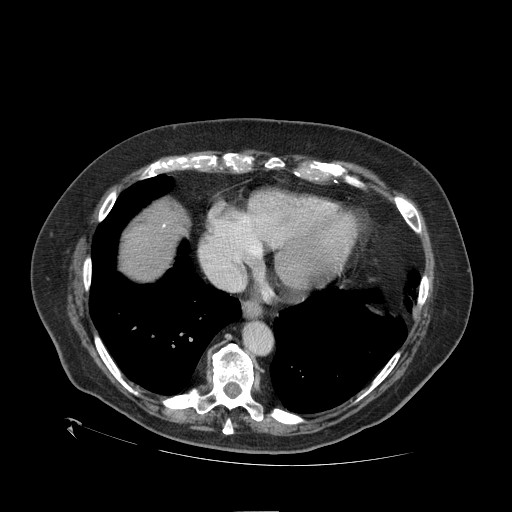
Contrast-enhanced abdominal CT (liver protocol), one axial slice. Slice 98 of 109 in the series (ordered by position). Reconstruction kernel STANDARD. 120 kVp. One of 2 acquisitions stored at this slice position. Soft-tissue window (W 400 / L 40 HU). 512 × 512 image matrix, field of view 460 × 460 mm. Case-level facts recorded for this patient, not image findings: diagnosis: hepatocellular carcinoma (patient treated with transarterial chemoembolisation; whether this scan precedes or follows treatment is not stated here); TNM stage (as recorded): Stage-I; Child-Pugh class: A; tumour differentiation: no biopsy; tumour size: 4.6 cm.
Structures marked on this image (semi-automatic segmentation, software-assisted and operator-edited):
- abdominal aorta: bounding box (x1, y1, x2, y2) in pixels: (244, 321, 272, 354)
- liver parenchyma outside the tumour (the mass and vessels are separate outlines, so this box may not span the whole liver): (120, 200, 188, 280)
- liver vessels: (163, 225, 165, 227)